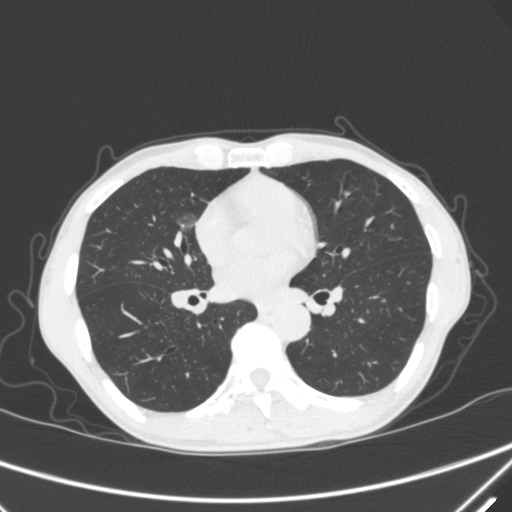
Chest CT, one axial slice. Slice 162 of 340 in the series (ordered by position). Lung window (W 1500 / L -600 HU). 1 mm slice thickness. 512 × 512 image matrix. Male patient, age 67 years. Case-level facts recorded for this patient, not image findings: clinical TNM (as recorded): T1c N0 M0.
Annotated regions visible in this slice (bounding box drawn by a radiologist):
- lung tumour (recorded histology: adenocarcinoma): bounding box [x1, y1, x2, y2] px = [174, 206, 200, 242]